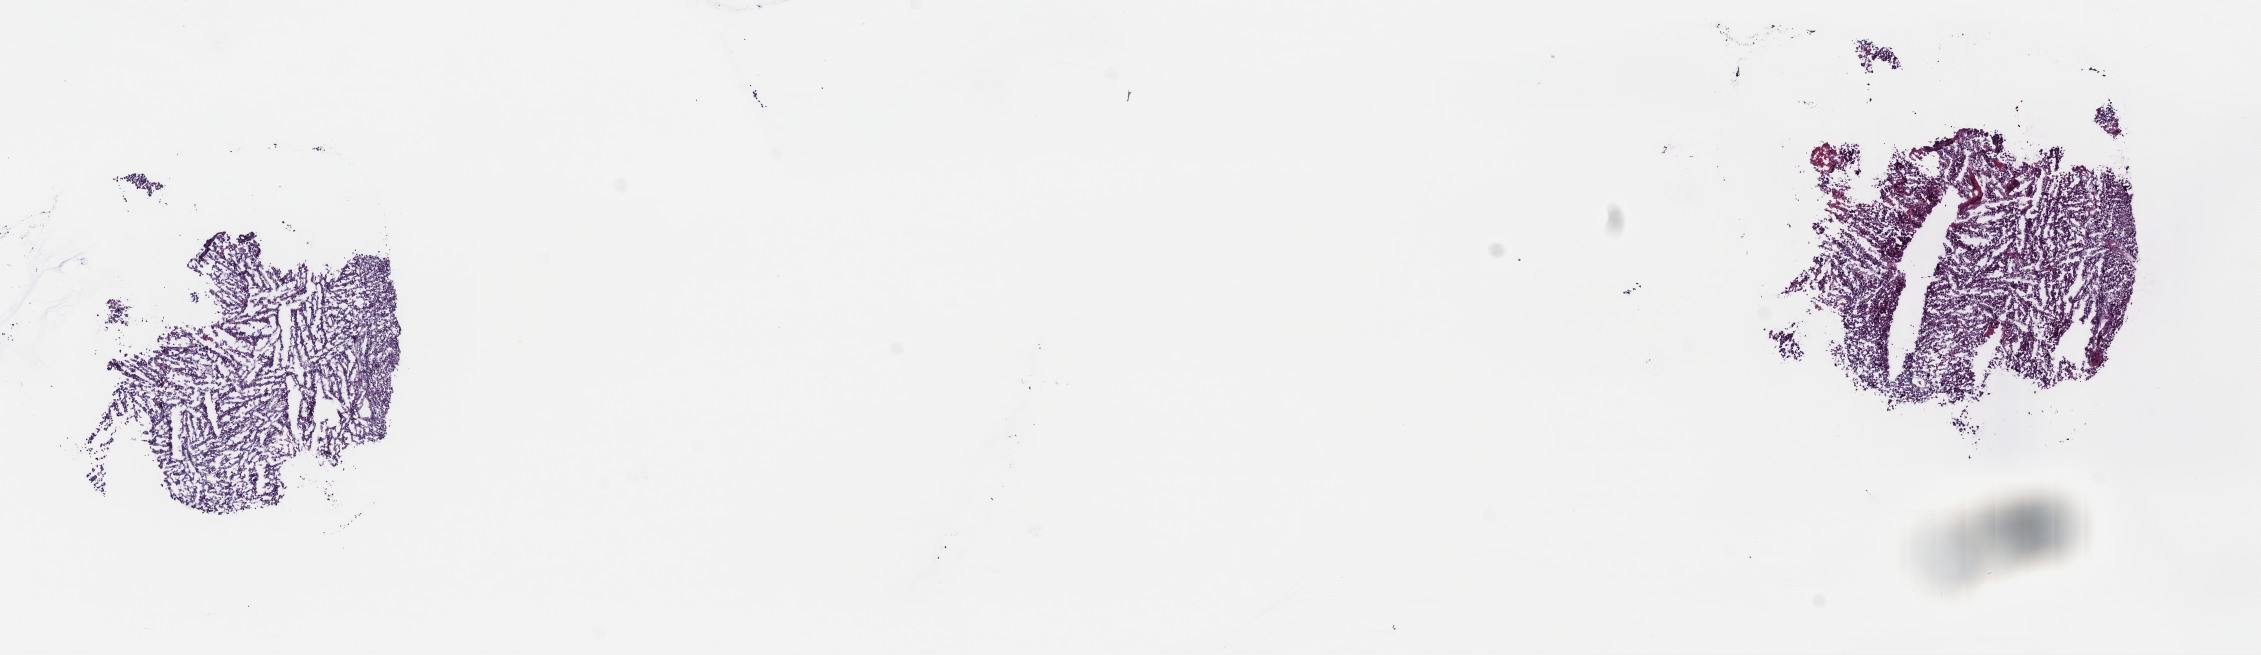
H&E whole-slide image — low-resolution overview of the scanned area, about 17.8 x 5.1 mm (from a 40x scan). Frozen section. Metastatic tumour sample, sampled site not recorded. Male patient; age at initial diagnosis 30 years. Composition of this section per pathologist review: tumour cells 90%, tumour nuclei 90%, normal cells 0%, stromal cells 5%, necrosis 5%. Inflammatory infiltration, as recorded: lymphocyte infiltration 5%, monocyte infiltration 0%, neutrophil infiltration 0%.
* this section: metastatic tumour tissue
* patient diagnosis: Malignant melanoma, NOS